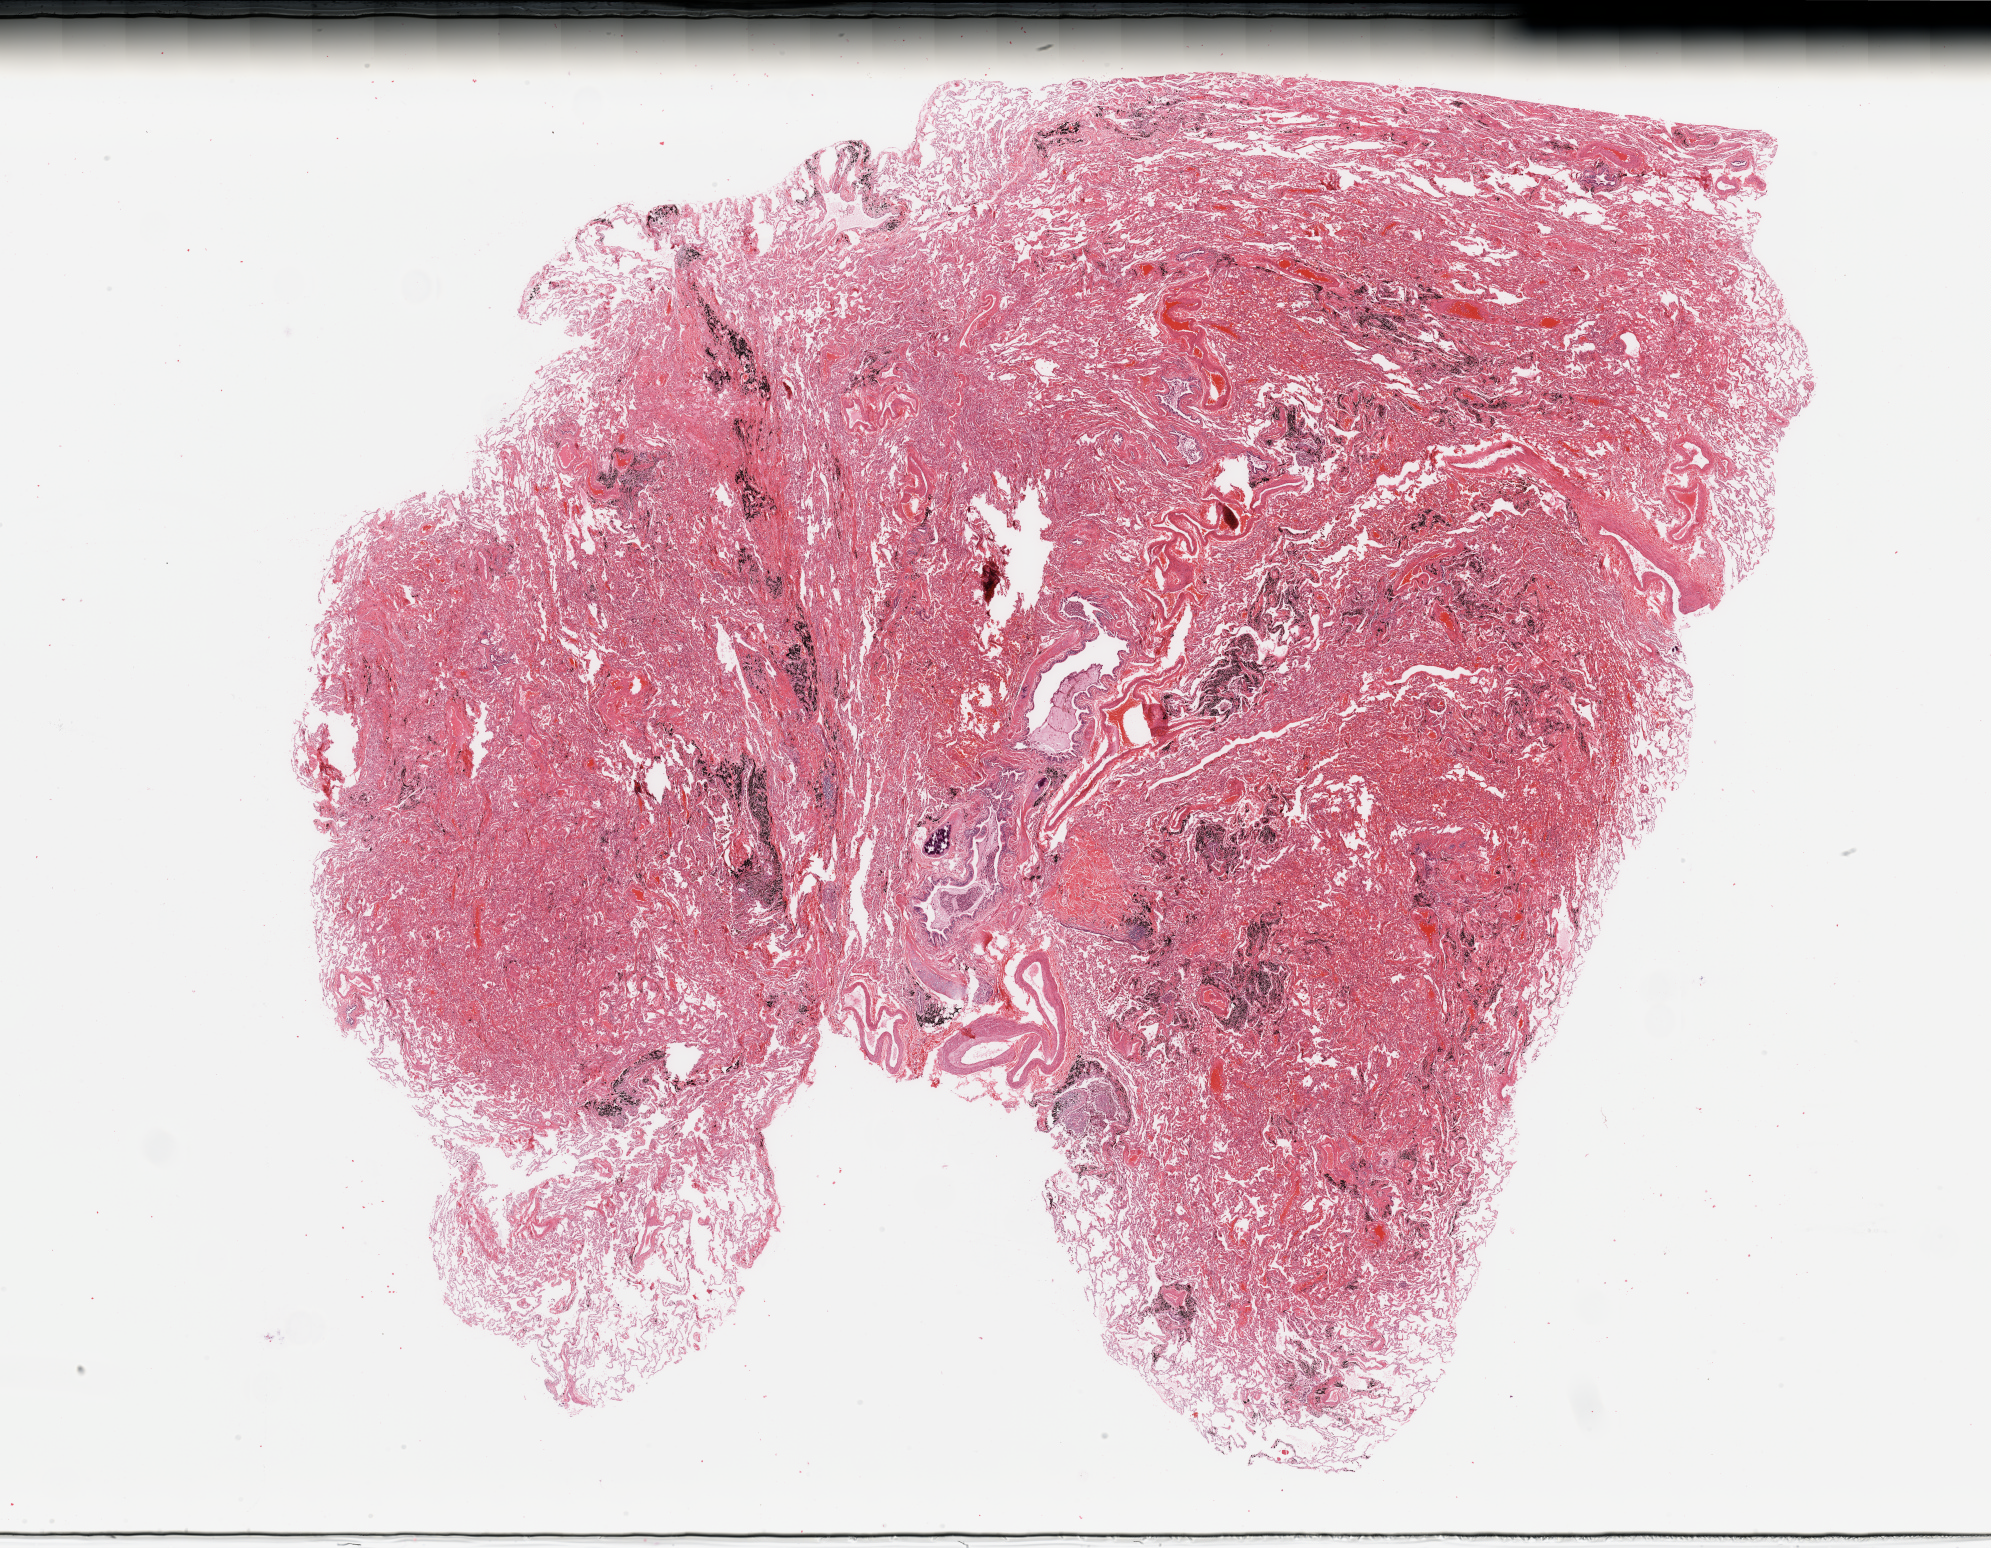
H&E whole-slide image, shown as a low-resolution overview of the whole scanned area (about 31.5 x 24.5 mm). Normal (non-tumour) tissue sample, lung. Patient: male, age 76 years.
This section: normal (non-tumour) tissue from the same patient. Patient diagnosis: Adenocarcinoma, NOS.